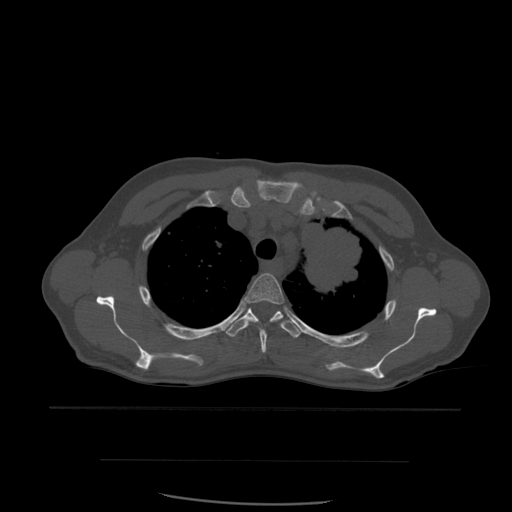
CT including the spine, one axial slice; position 435 of 574 along the scan axis; bone window (W 1800 / L 400 HU); 1.25 mm slice thickness; 512 × 512 image matrix, field of view 392 × 392 mm. Patient age 48 years. Case-level facts recorded for this patient, not image findings: primary cancer: lung; vertebrae with lytic lesions (as recorded): T11.
Structures marked on this image (semi-automatic segmentation, software-assisted and operator-edited):
- T3 vertebra: bounding box <244,273,284,353> (left, top, right, bottom; pixels)
- T4 vertebra: <226,308,303,339>
- T5 vertebra: <276,299,284,304>